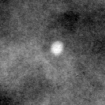
Crop from a digitized film mammogram around one marked abnormality; right breast; CC view; BI-RADS breast density category 3 (scale 1–4).
- Finding: calcifications, morphology round and regular / lucent center; BI-RADS assessment category 2; benign; no additional work-up was recommended (benign without callback).